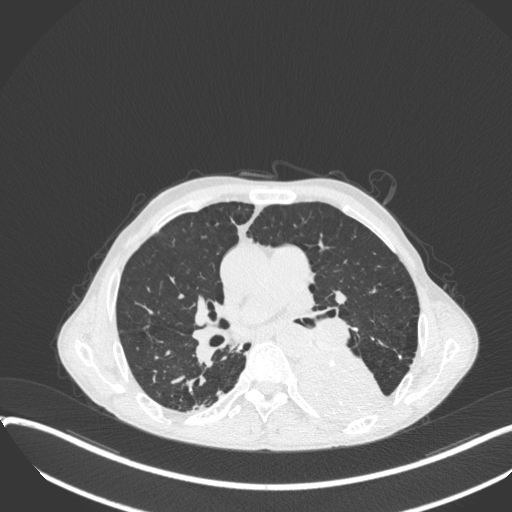
Chest CT, one axial slice; slice 211 of 400 in the series (ordered by position); reconstruction kernel B31f; lung window (W 1500 / L -600 HU); 512 × 512 image matrix. Male patient, age 57 years. Case-level facts recorded for this patient, not image findings: clinical TNM (as recorded): T4 N0 M0.
Structures marked on this image (rectangle marked by the reading radiologist):
- lung tumour (recorded histology: squamous cell carcinoma): box from (x=285, y=342) to (x=389, y=425) px